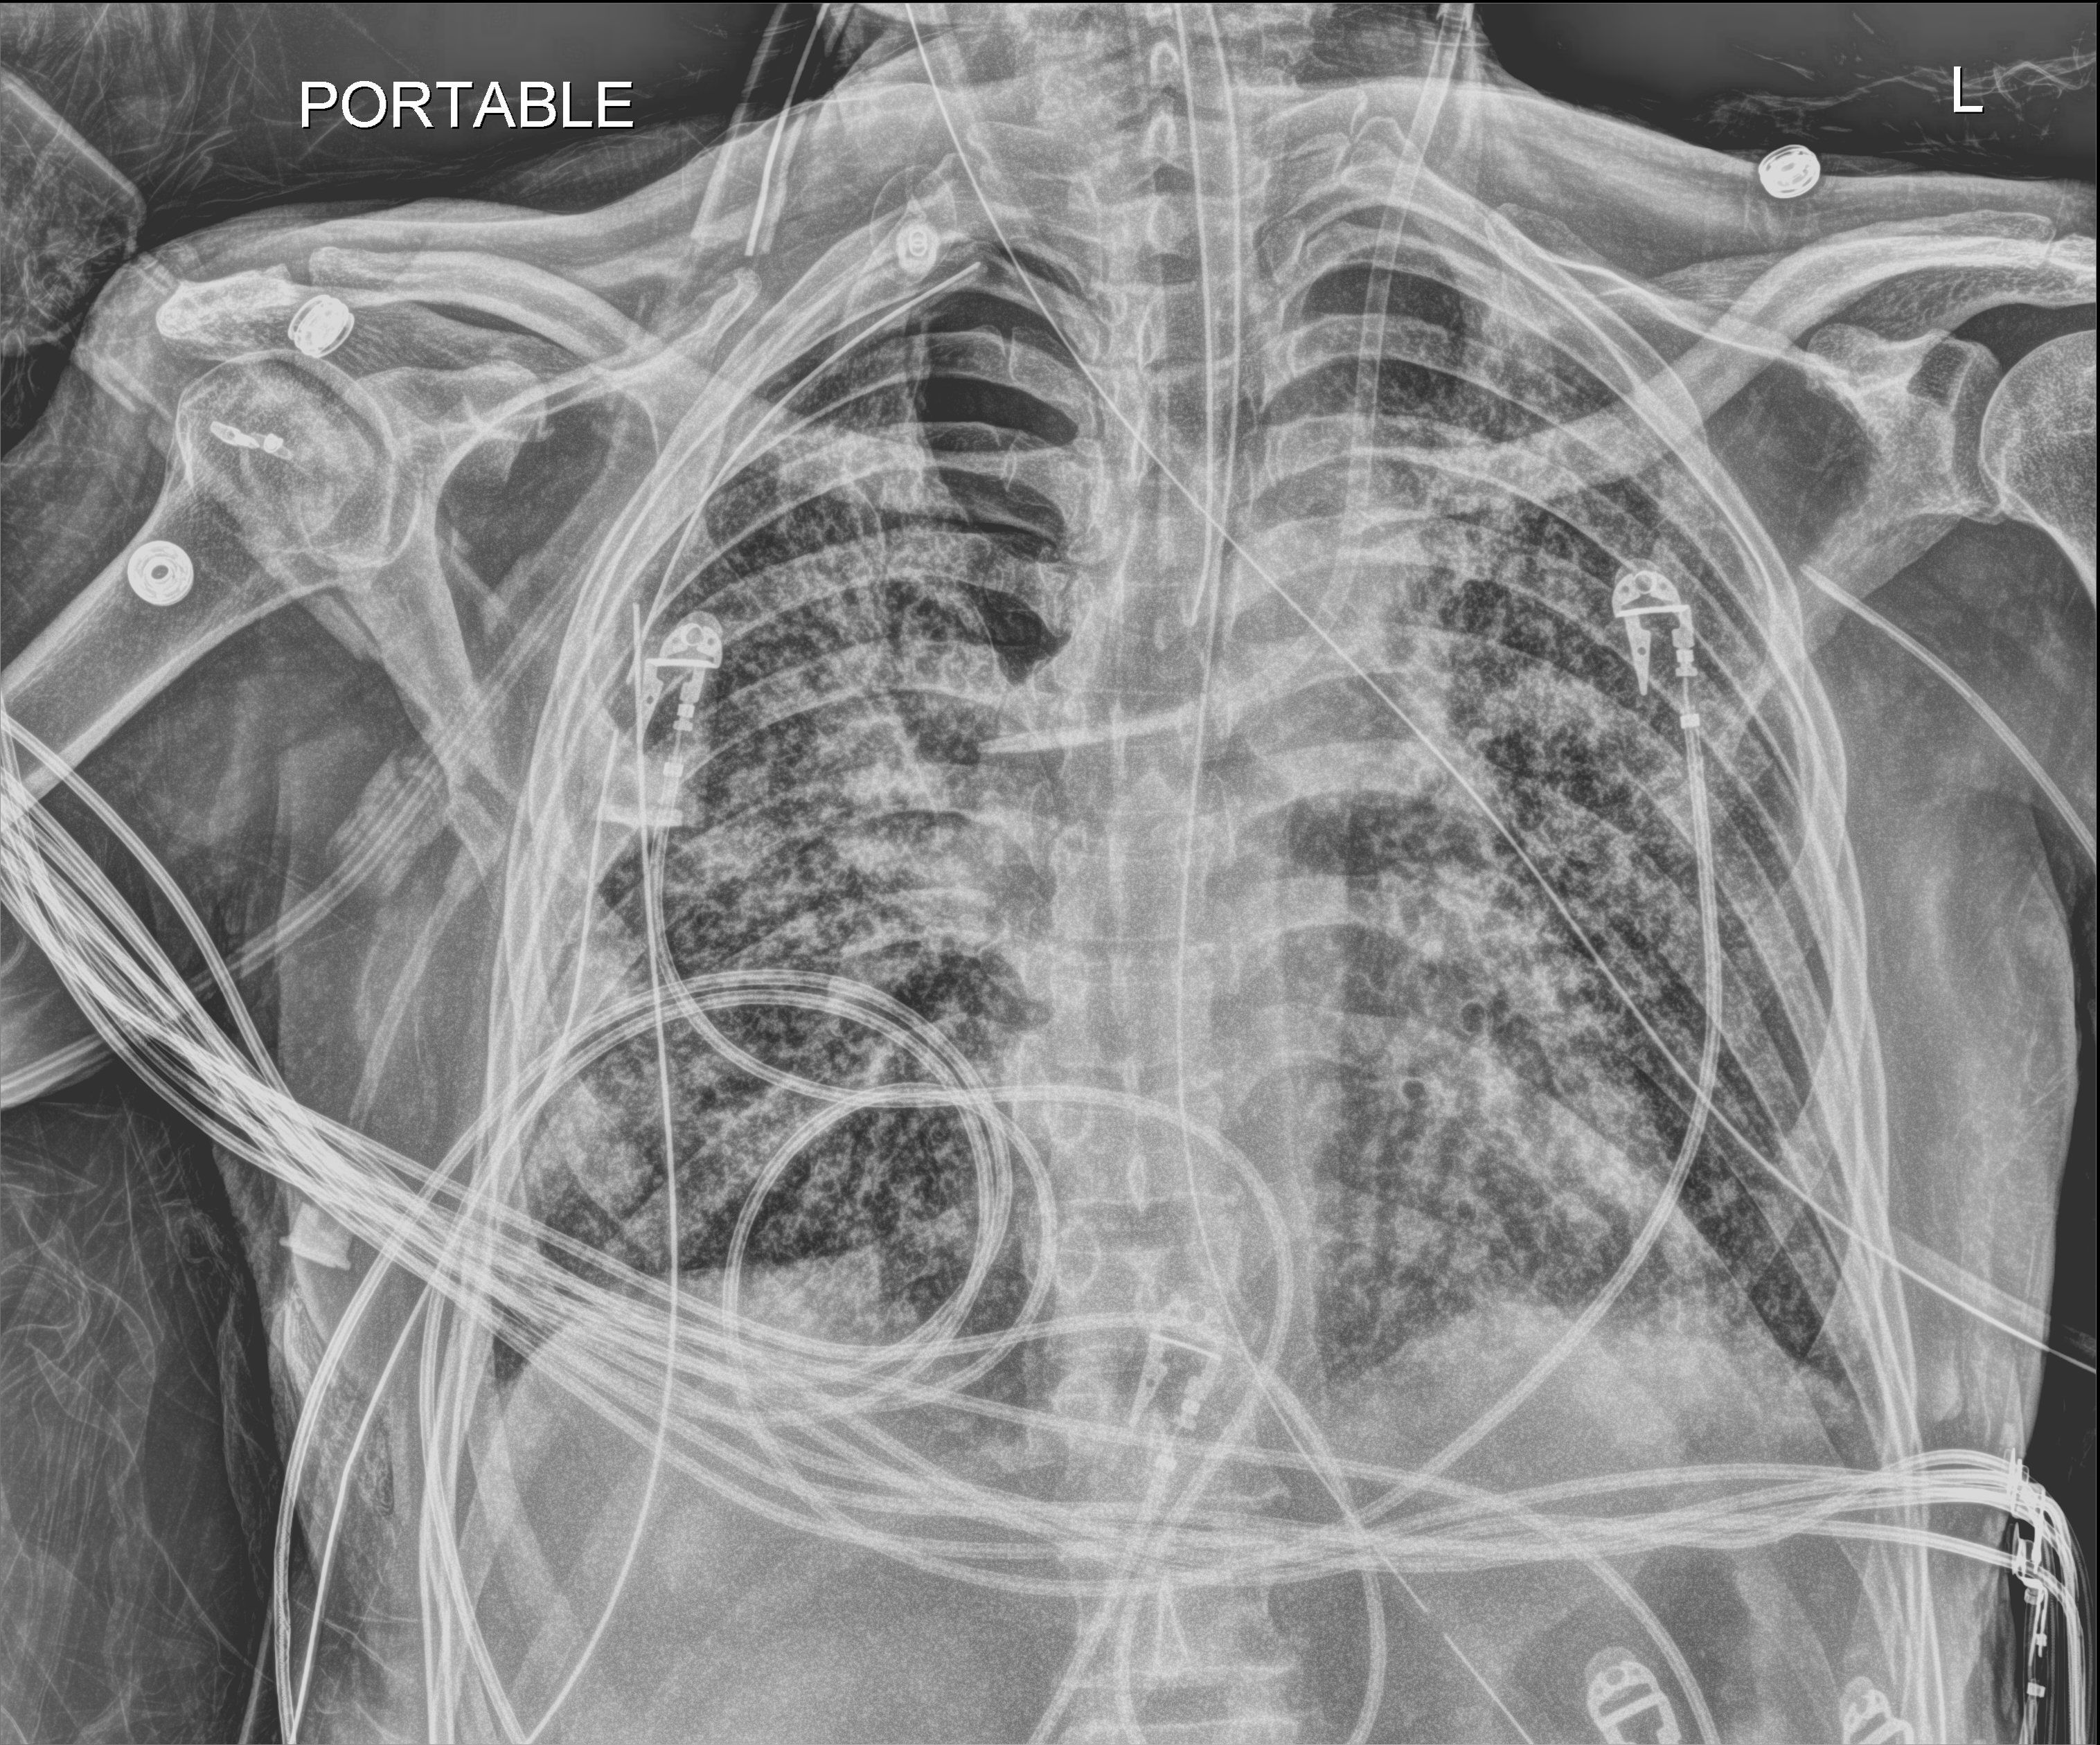
Chest radiograph (digital radiography), anteroposterior (AP) projection. Patient hospitalised with COVID-19; male, aged 60–74 years.
Admission-level facts for this patient (not findings on this image; timing relative to this image not recorded): admitted to intensive care during this hospital stay: yes; mechanically ventilated during this hospital stay: yes.